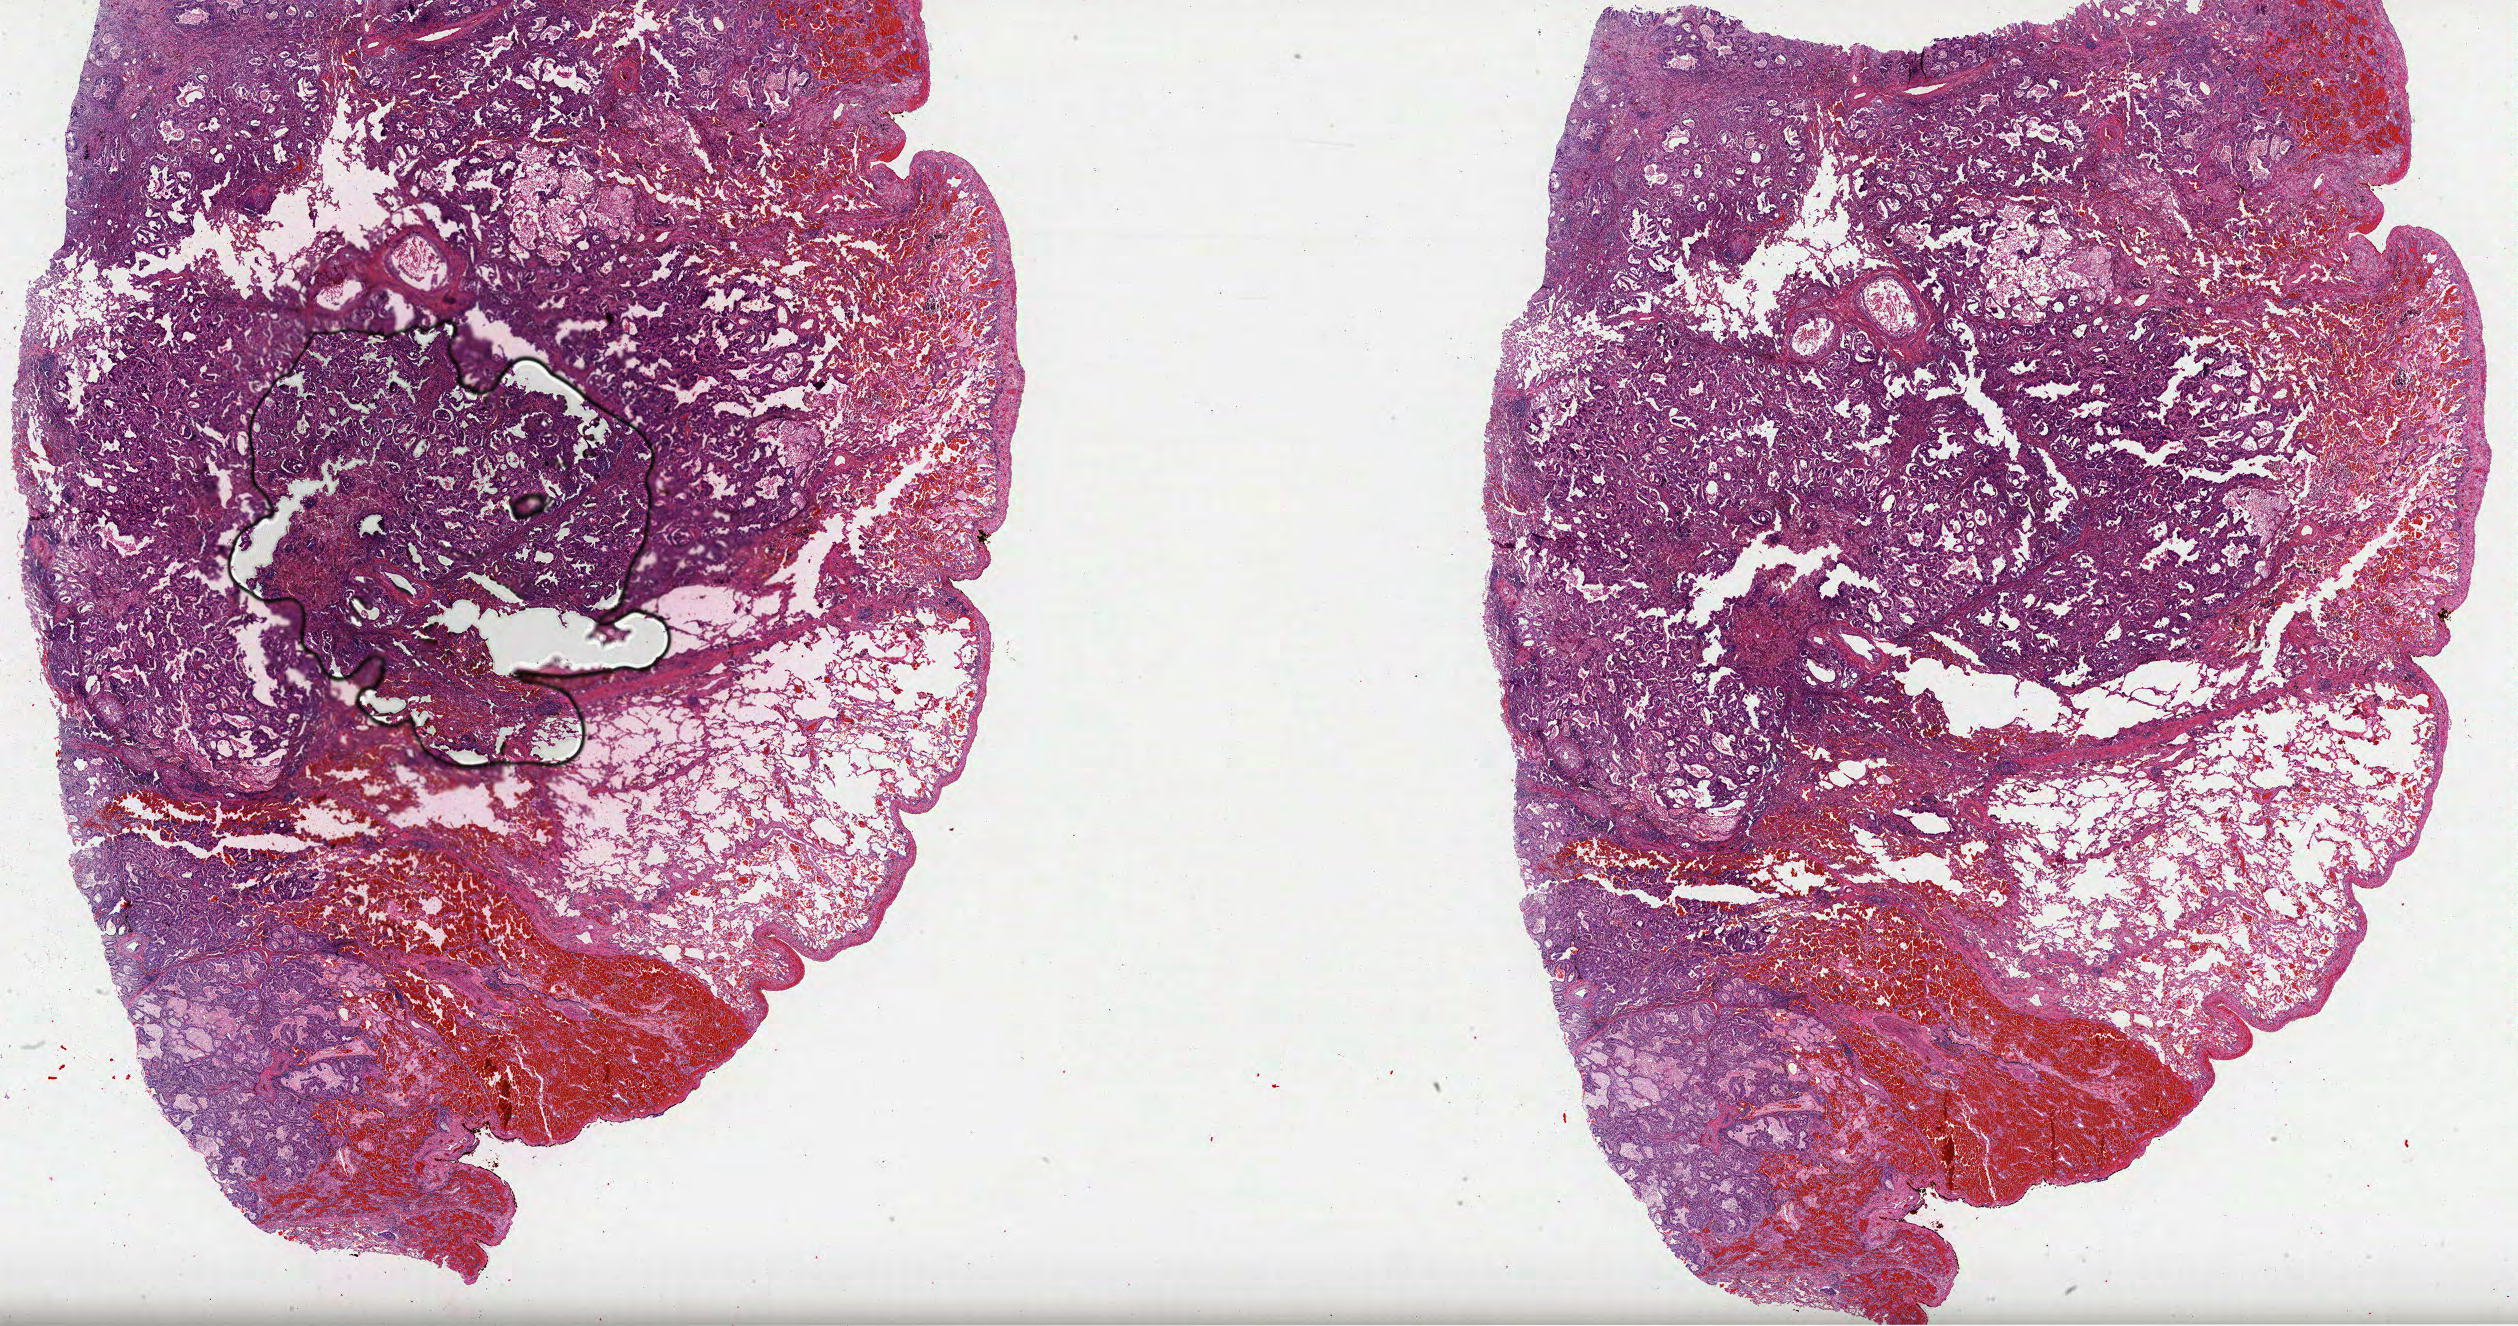
Digitized Hematoxylin and eosin (H&E) stained tissue section (whole slide) — whole scanned area (about 40.6 x 21.4 mm, slide scanned at 40x) shown as a low-resolution overview. Formalin-fixed paraffin-embedded (FFPE) diagnostic section. Lung, primary tumour sample. Male patient; age at initial diagnosis 70 years.
Diagnosis: Mucinous adenocarcinoma (upper lobe, lung). Laterality: left. AJCC pathologic stage: IIA (7th edition).